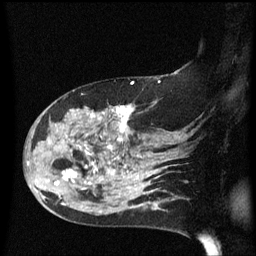
Breast MRI (dynamic contrast-enhanced), one sagittal slice. Slice 39 of 60 in the series (ordered by position). Dynamic contrast-enhanced series, image 2 of 3 at this slice position (ordered by acquisition). 1.5 T. TE 4.2 ms, TR 8.4 ms. 2.2 mm slice thickness. 256 × 256 image matrix, field of view 200 × 200 mm. Patient: female, 47 years.
Annotated regions visible in this slice (semi-automatic segmentation, software-assisted and operator-edited):
- analysis volume of interest (the breast-tissue region the enhancement analysis was run in; not a lesion): bounding box [x1, y1, x2, y2] px = [24, 97, 149, 206]
- tumour enhancement mask (voxels above the 70 % enhancement threshold inside the analysis volume of interest): [28, 106, 149, 200]